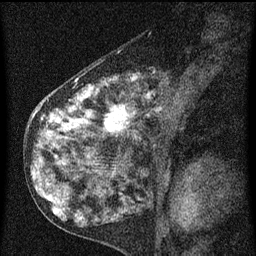
Breast MRI (dynamic contrast-enhanced), one sagittal slice; position 31 of 60 along the scan axis; dynamic contrast-enhanced series, image 2 of 3 at this slice position (ordered by acquisition); 1.5 T; TE 4.2 ms, TR 8 ms; 256 × 256 image matrix, field of view 180 × 180 mm. Female patient, age 55 years.
Outlined on this slice (semi-automatically segmented with operator editing):
- analysis volume of interest (the breast-tissue region the enhancement analysis was run in; not a lesion): bounding box <42,72,185,155> (left, top, right, bottom; pixels)
- tumour enhancement mask (voxels above the 70 % enhancement threshold inside the analysis volume of interest): <44,78,162,135>